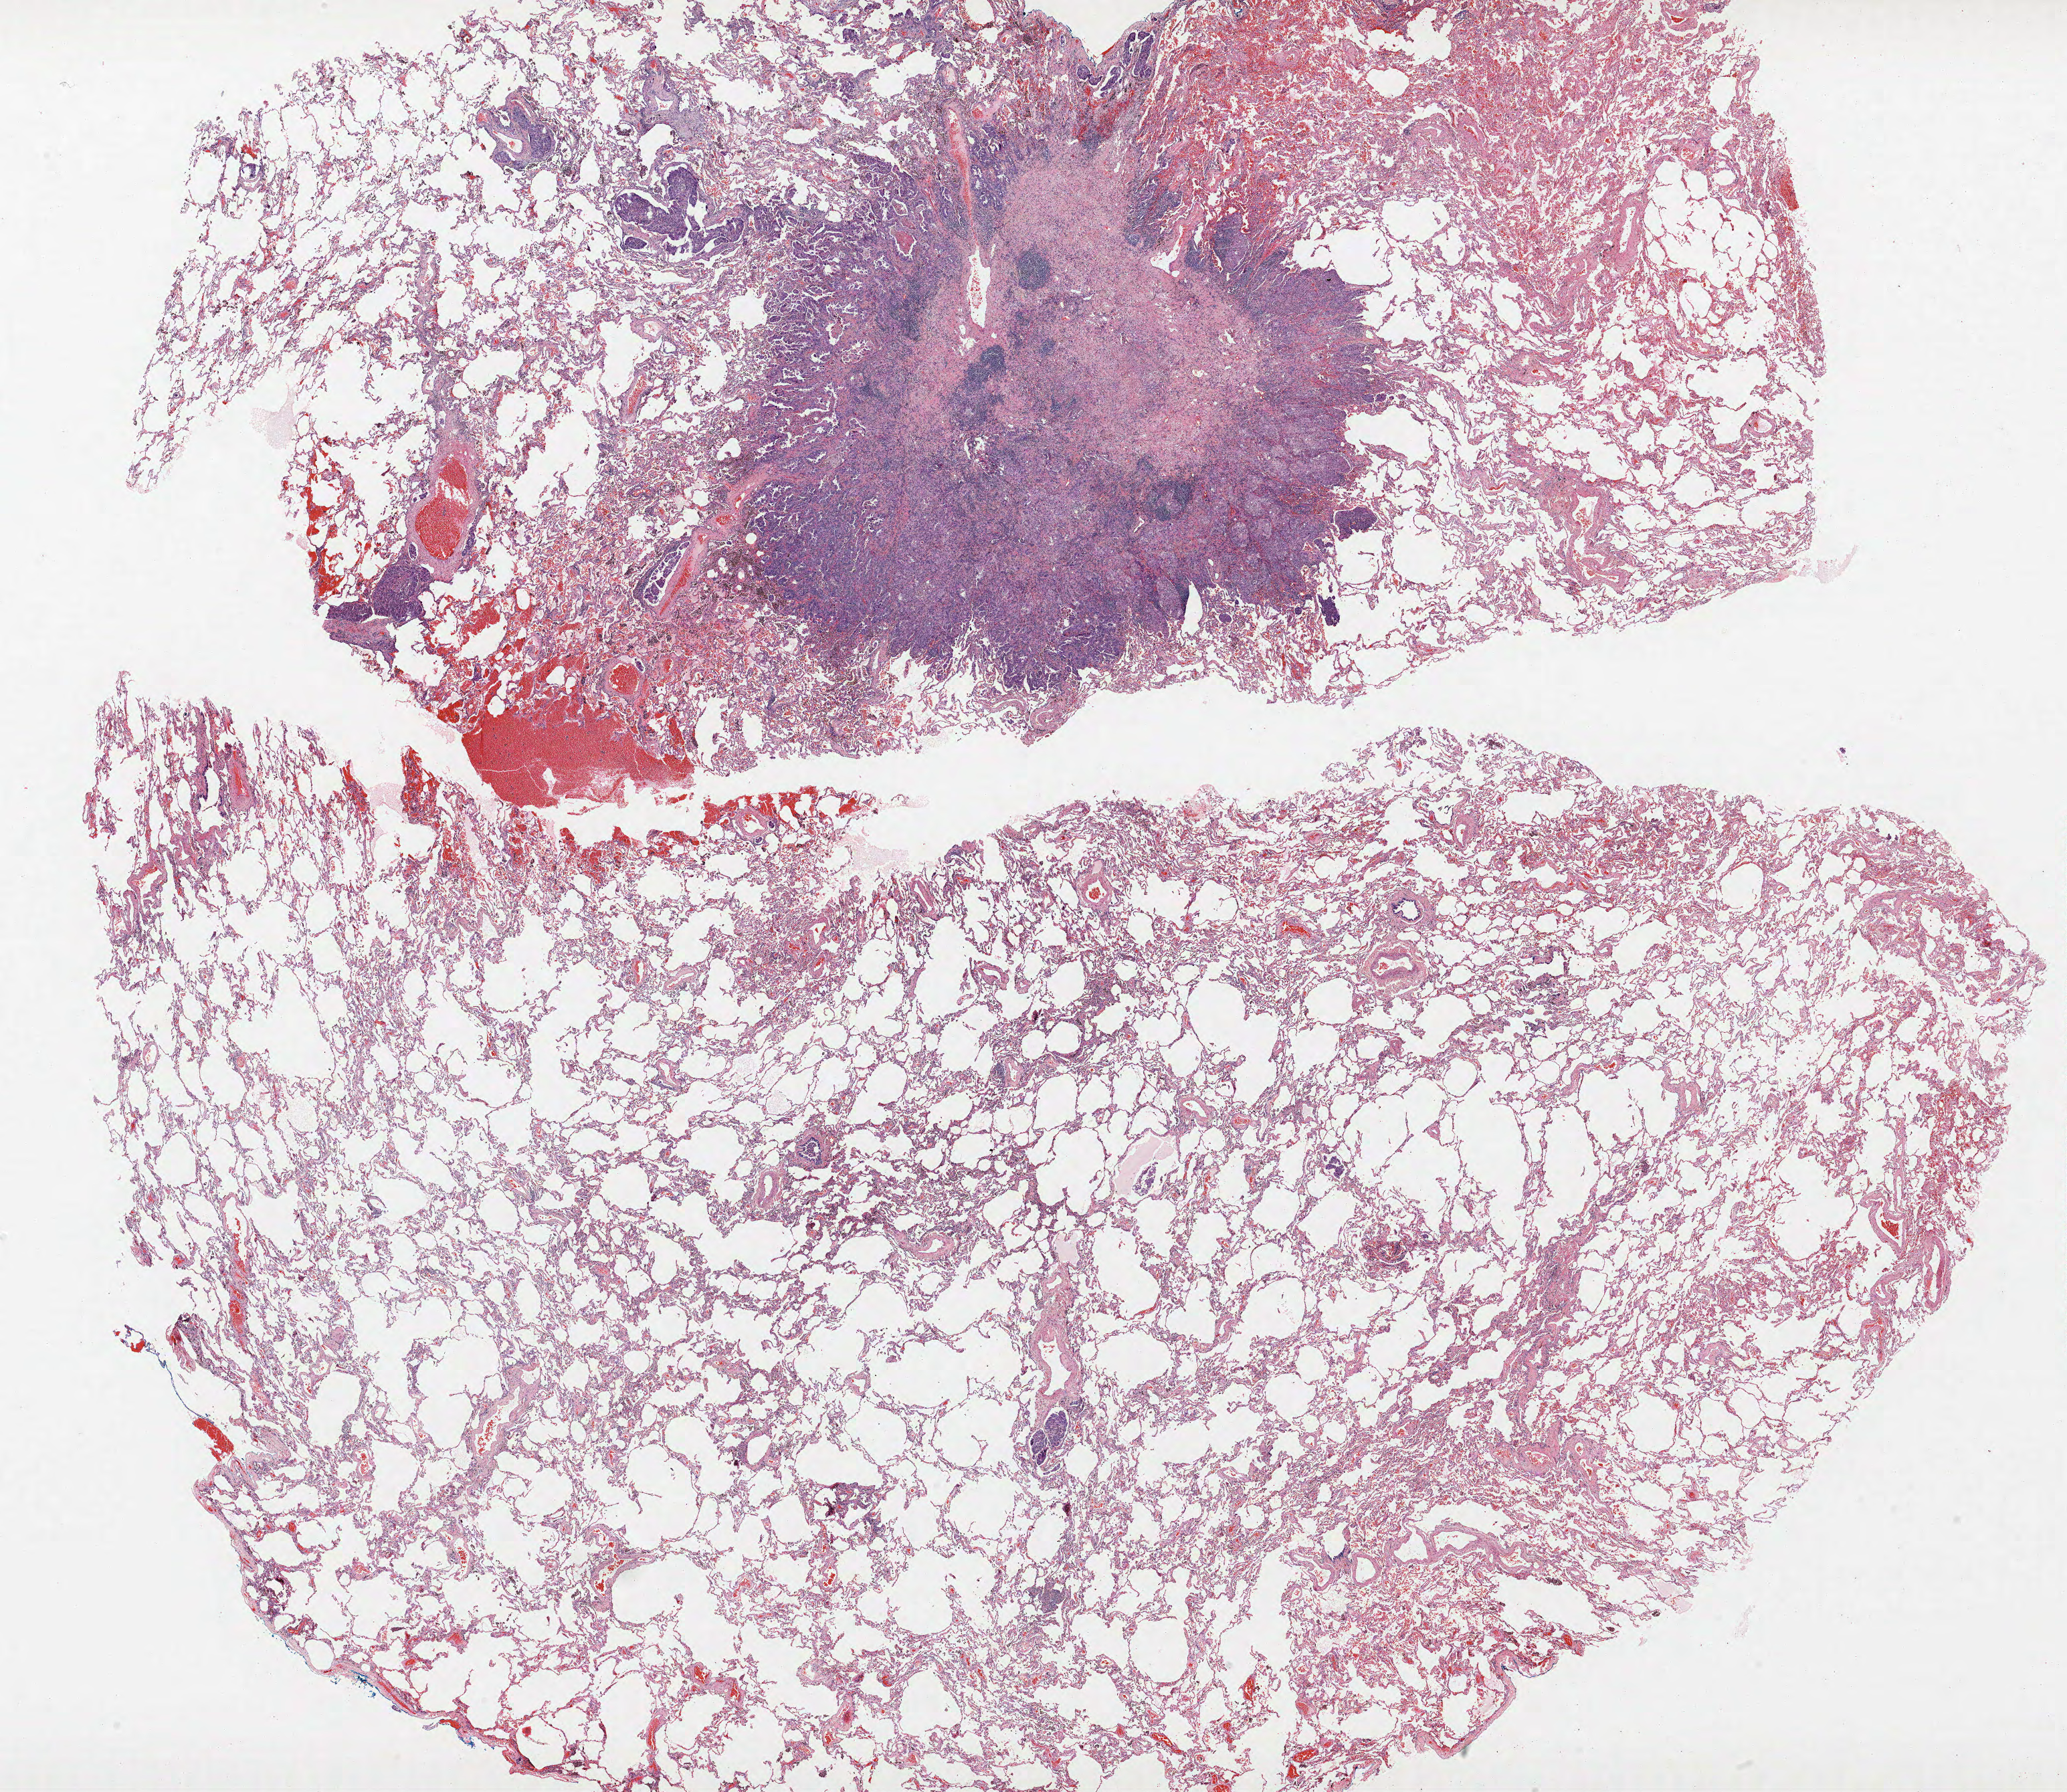
Hematoxylin and eosin (H&E) stained whole-slide image — shown as a low-resolution overview of the whole scanned area (about 24.7 x 21.4 mm). Formalin-fixed paraffin-embedded (FFPE) section. Lung tissue. Male, age 60 at enrolment. Current smoker at enrolment. Grade: poorly differentiated (G3).
Tumour size (pathology): 20 mm. Participant's lung-cancer diagnosis: Adenocarcinoma, NOS. Stage (AJCC 6th edition): IIIA. Primary tumour location (clinical record): left upper lobe.